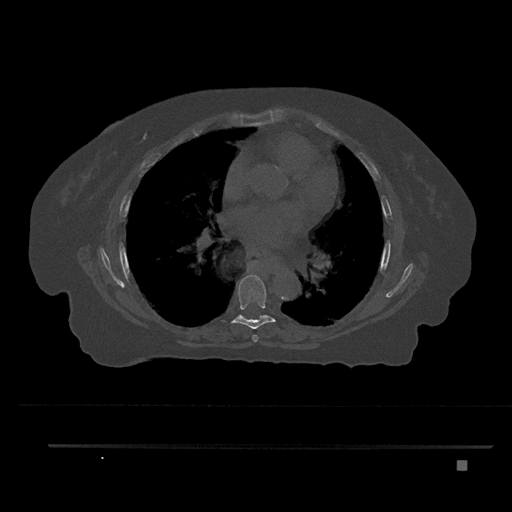
CT including the spine, one axial slice; slice 487 of 797 in the series (ordered by position); 120 kVp; bone window (W 1800 / L 400 HU); 512 × 512 image matrix, field of view 437 × 437 mm. Female patient, age 76 years. Case-level facts recorded for this patient, not image findings: primary cancer: lung; vertebrae with lytic lesions (as recorded): T11, L3.
Structures marked on this image (semi-automatic segmentation, software-assisted and operator-edited):
- T6 vertebra: bounding box (x1, y1, x2, y2) in pixels: (252, 334, 259, 342)
- T7 vertebra: (222, 274, 277, 329)
- T8 vertebra: (240, 315, 268, 320)